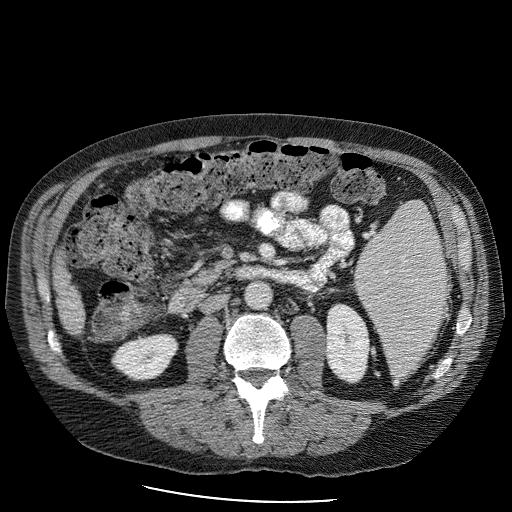
Contrast-enhanced abdominal CT (liver protocol), one axial slice. Position 23 of 98 along the scan axis. Reconstruction kernel STANDARD. 120 kVp. Soft-tissue window (W 400 / L 40 HU). 2.5 mm slice thickness. 512 × 512 image matrix, field of view 400 × 400 mm. Case-level facts recorded for this patient, not image findings: diagnosis: hepatocellular carcinoma (patient treated with transarterial chemoembolisation; whether this scan precedes or follows treatment is not stated here); TNM stage (as recorded): Stage-II; Child-Pugh class: B; tumour differentiation: moderately differentiated; tumour nodularity: uninodular.
Structures marked on this image (semi-automatically segmented with operator editing):
- liver parenchyma outside the tumour (the mass and vessels are separate outlines, so this box may not span the whole liver): bounding box (x1, y1, x2, y2) in pixels: (52, 232, 84, 333)